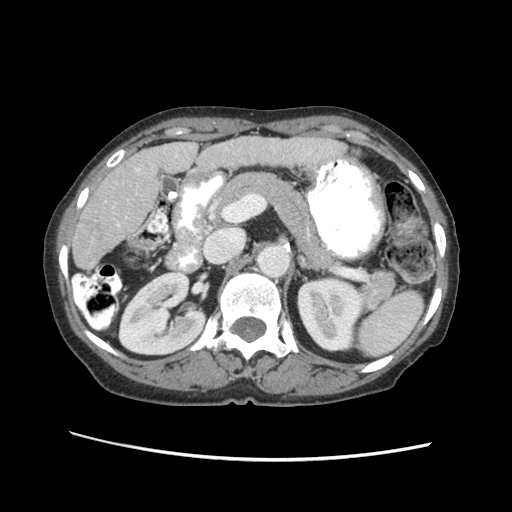
Contrast-enhanced abdominal CT (liver protocol), one axial slice. Position 24 of 63 along the scan axis. Reconstruction kernel STANDARD. 120 kVp. Soft-tissue window (W 400 / L 40 HU). 2.5 mm slice thickness. 512 × 512 image matrix, field of view 340 × 340 mm. From the clinical record (not read from this slice): diagnosis: hepatocellular carcinoma (patient treated with transarterial chemoembolisation; whether this scan precedes or follows treatment is not stated here); TNM stage (as recorded): Stage-I; Child-Pugh class: B.
Annotated regions visible in this slice (semi-automatically segmented with operator editing):
- liver parenchyma outside the tumour (the mass and vessels are separate outlines, so this box may not span the whole liver): bounding box (x1, y1, x2, y2) in pixels: (70, 132, 341, 268)
- liver vessels: (133, 152, 174, 169)